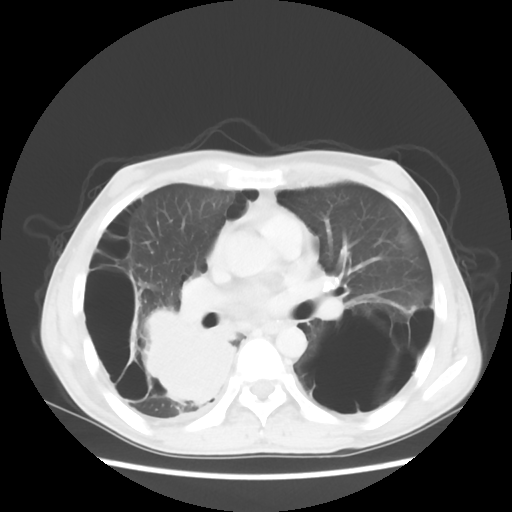
Chest CT, one axial slice. Position 29 of 56 along the scan axis. Lung window (W 1500 / L -600 HU). 5 mm slice thickness. 512 × 512 image matrix. Patient: male, 41 years. From the clinical record (not read from this slice): clinical TNM (as recorded): T4 N0 M1a.
Annotated regions visible in this slice (bounding box drawn by a radiologist):
- lung tumour (recorded histology: large cell carcinoma): bounding box <129,296,253,423> (left, top, right, bottom; pixels)